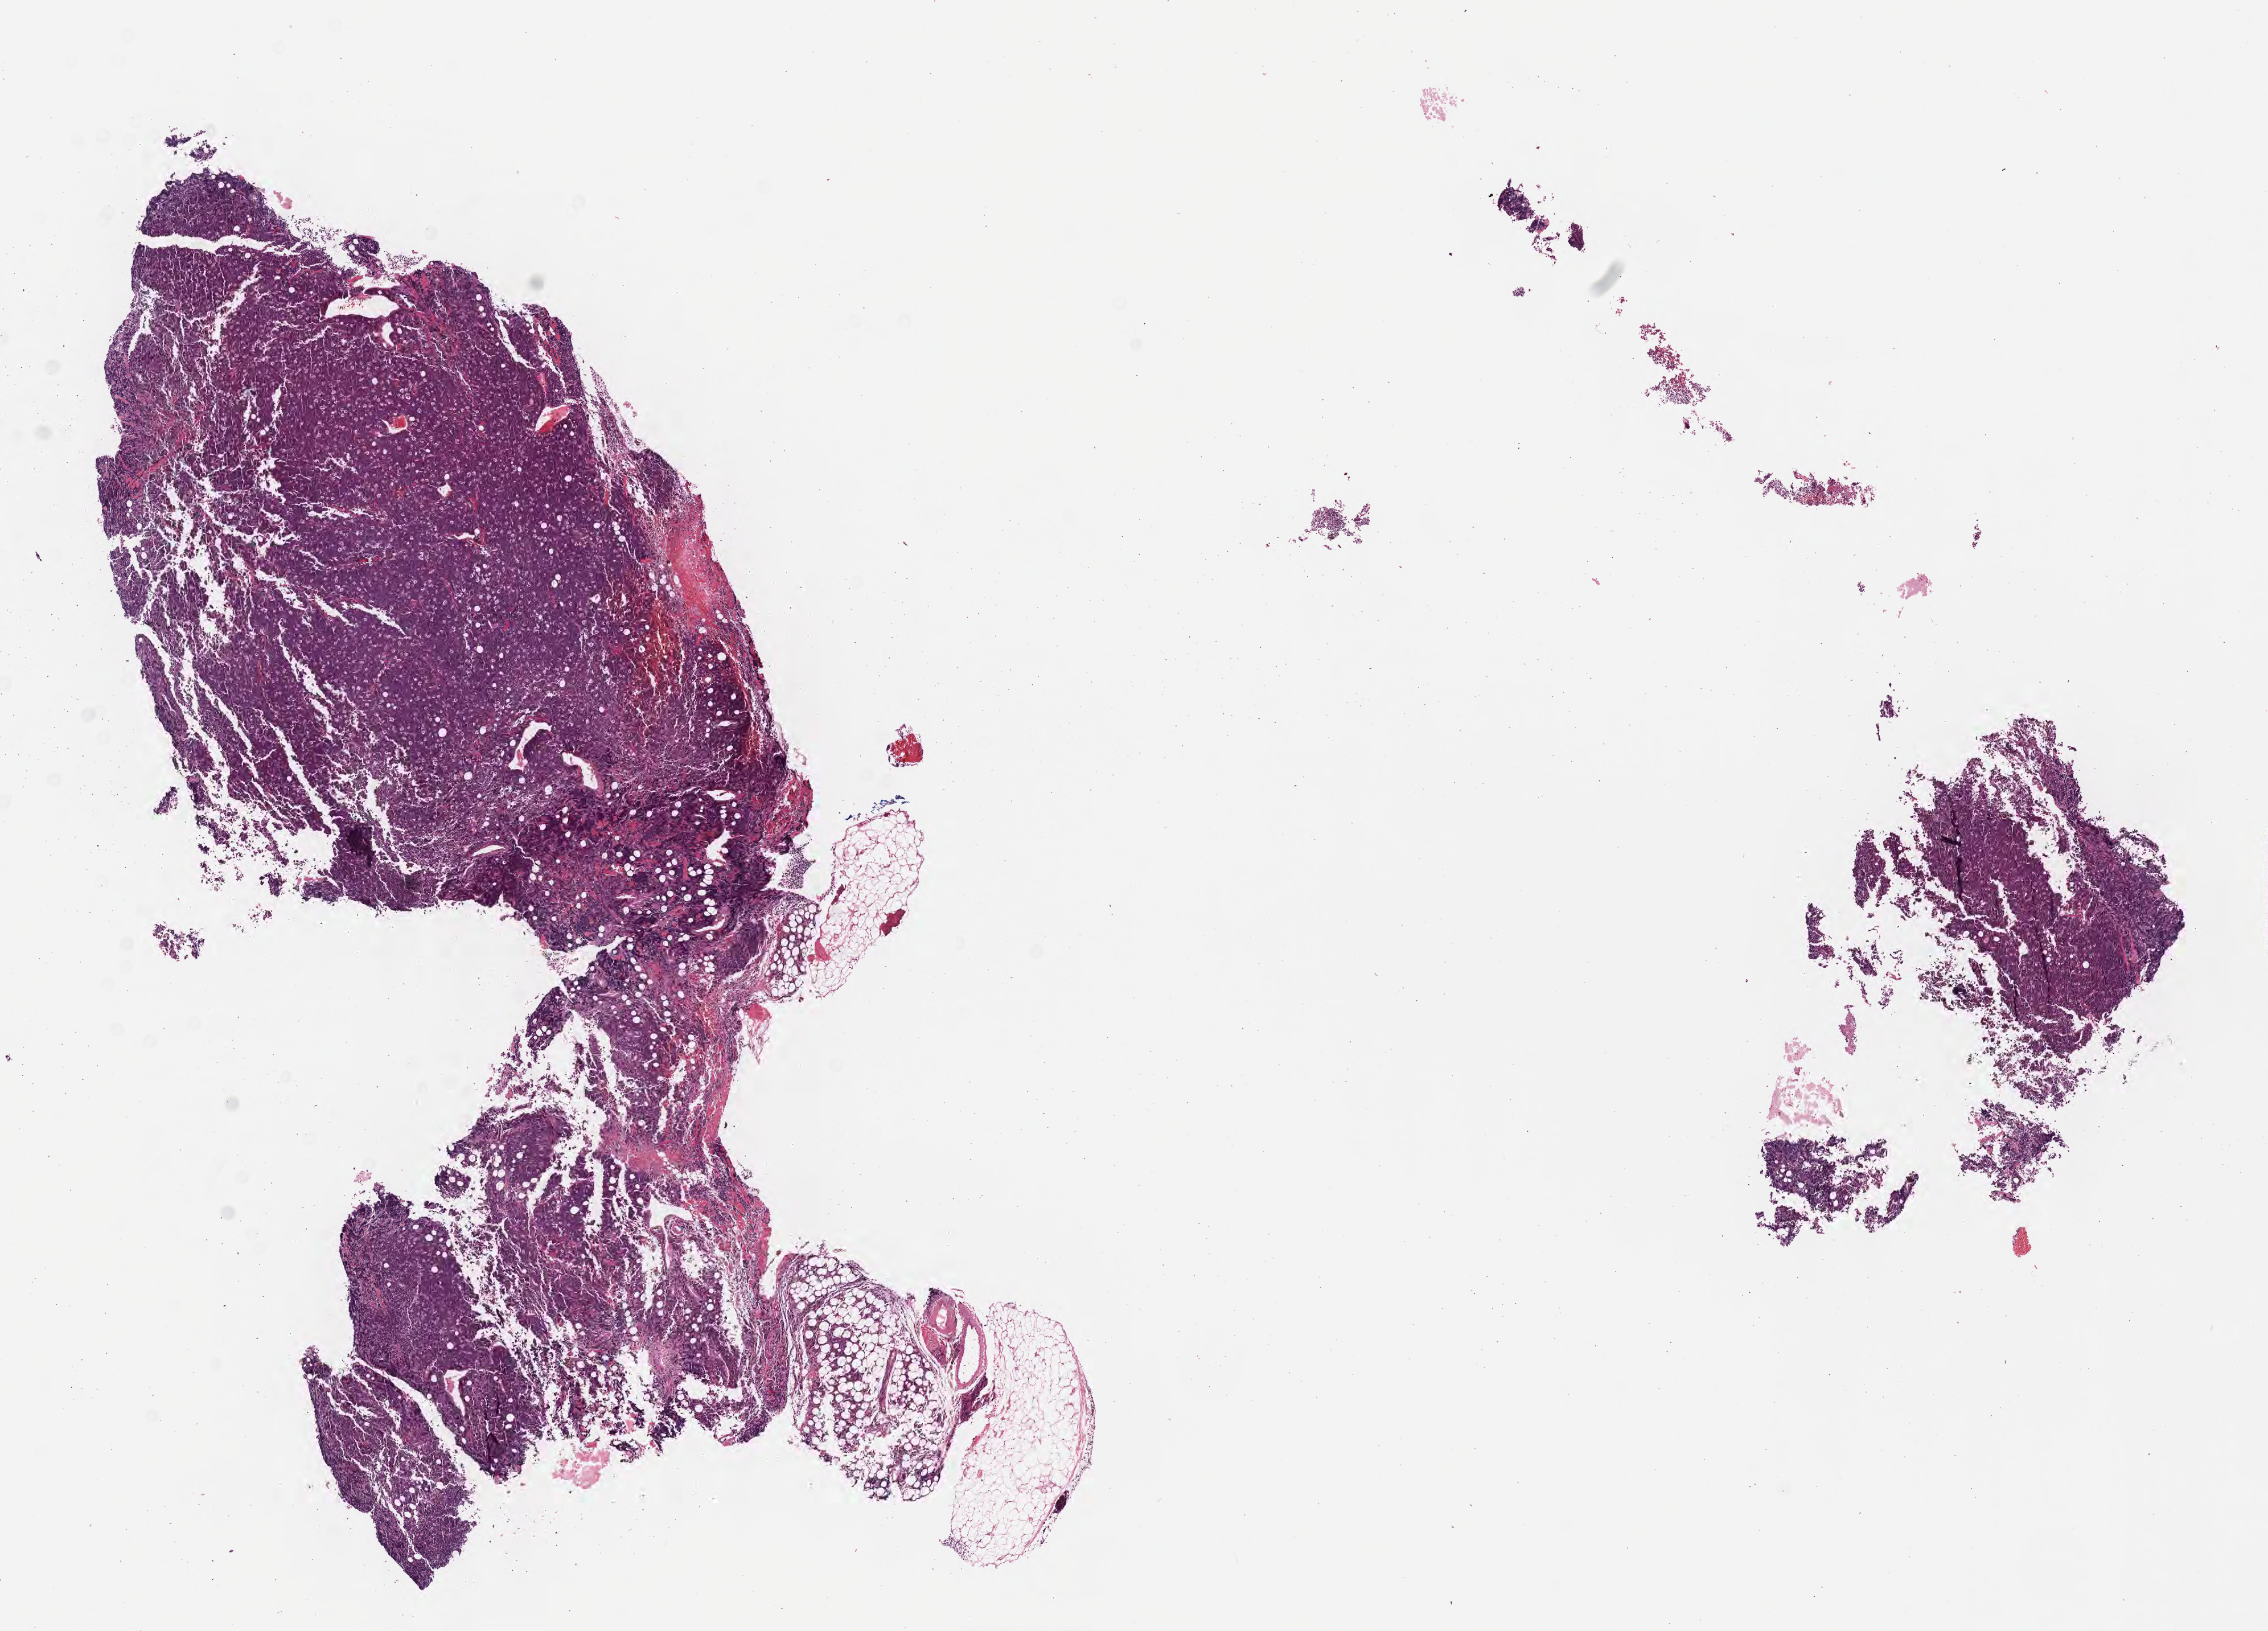
Whole-slide image, H&E stain, shown as a low-resolution overview of the whole scanned area (about 16.1 x 11.6 mm); FFPE section; primary tumor. Patient: female, 16 years old. Composition of this section per pathologist review: tumor cells 90%, tumor nuclei 95%, stromal cells 5%, necrosis 0%, normal cells 5%. Infiltration values recorded for this section: lymphocyte infiltration 50%, monocyte infiltration 25%, neutrophil infiltration 0%.
Histologic diagnosis: Burkitt lymphoma, NOS. Section: bottom of the tissue portion. Ann Arbor stage (patient): Stage IV.